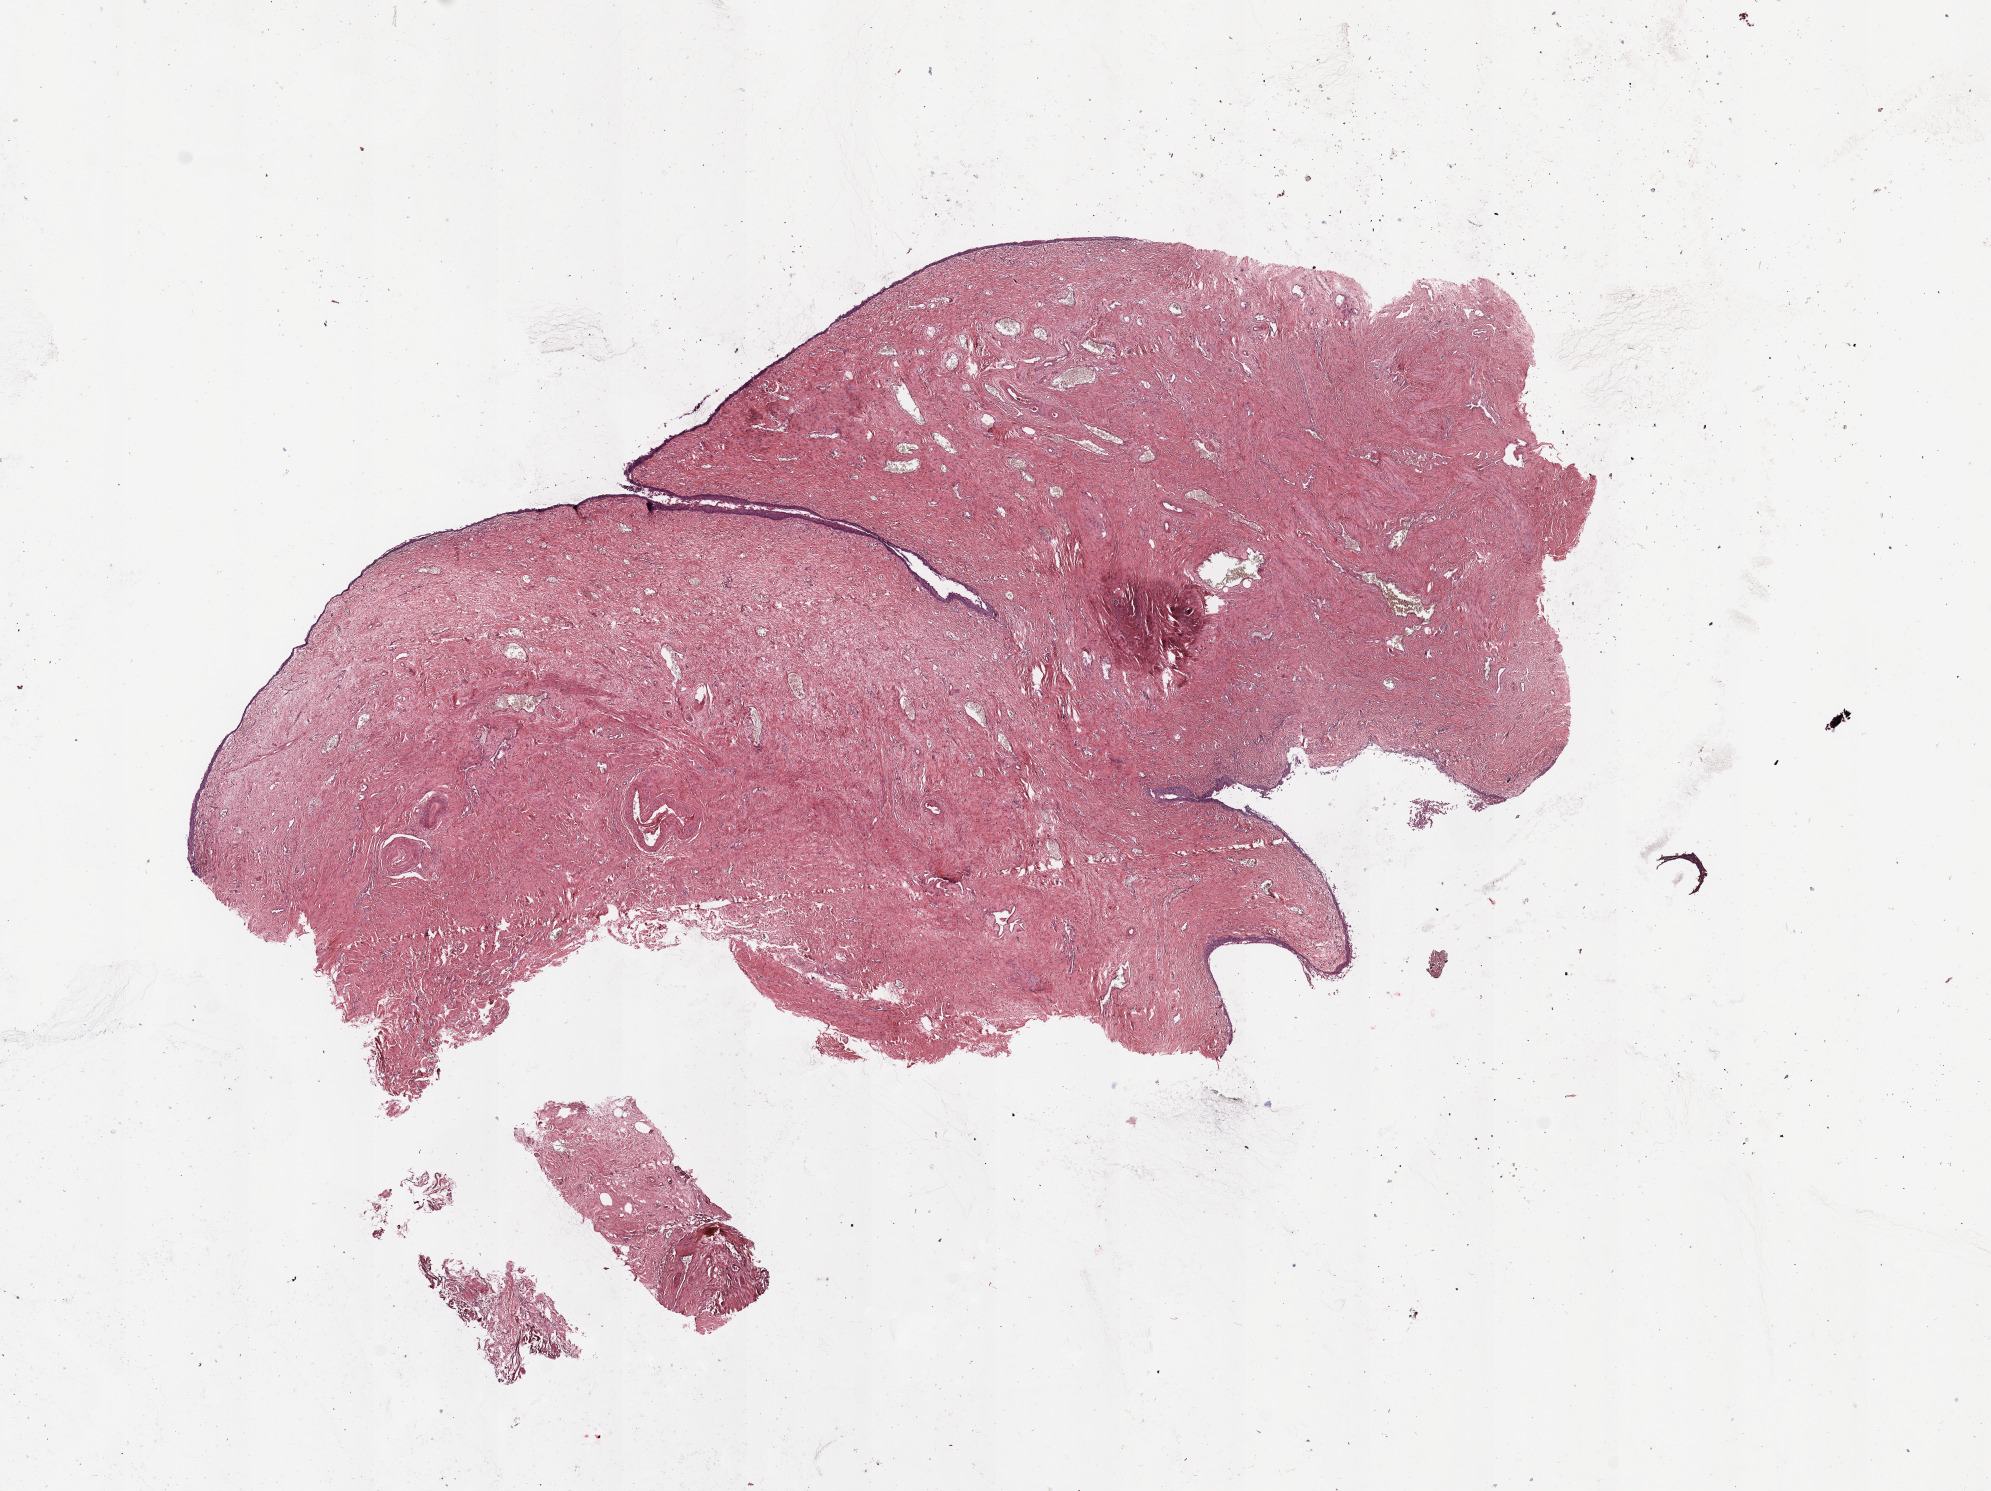
Digitized H&E-stained tissue section (whole slide) — whole scanned area (about 15.8 x 11.8 mm, slide scanned at 20x) shown as a low-resolution overview; normal (non-tumour) tissue sample, sampled site: uterus. Patient: female, age 77 years.
This section: normal (non-tumour) tissue from the same patient. Patient diagnosis: Endometrioid adenocarcinoma, NOS.